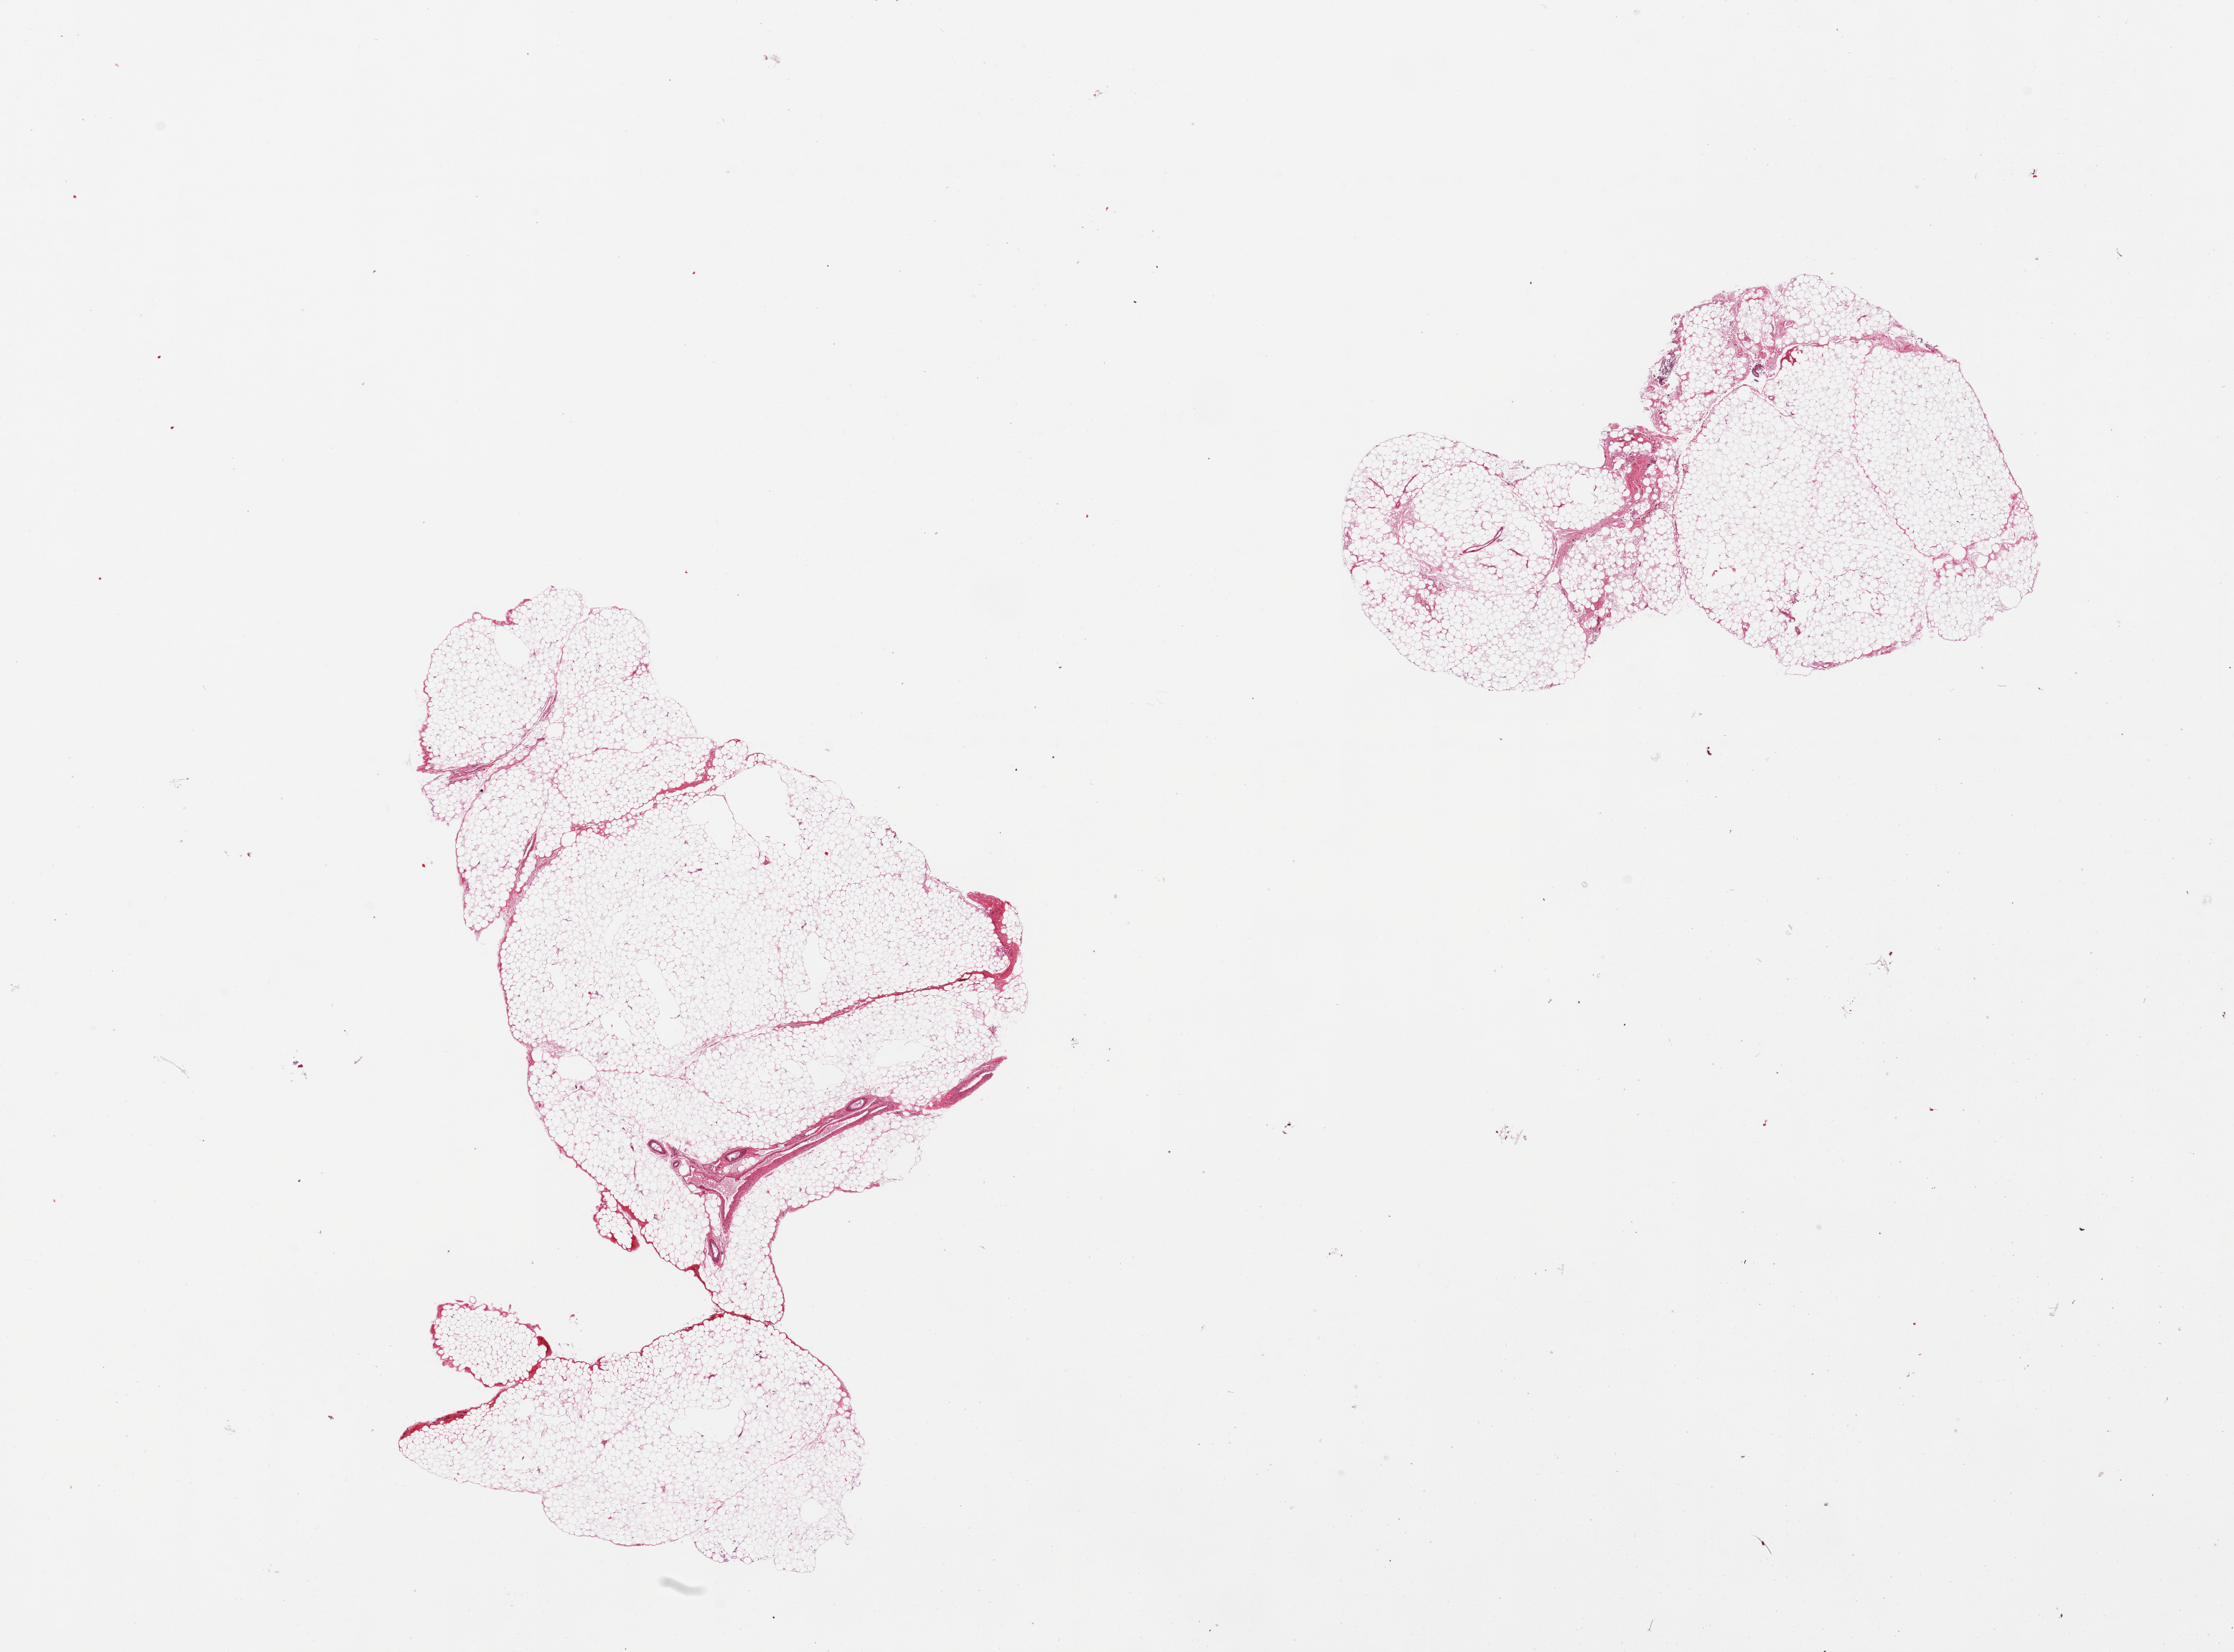
Hematoxylin and eosin (H&E) whole-slide image — a low-resolution overview of the entire scanned area, about 24.6 x 18.2 mm; PAXgene-fixed, paraffin-embedded tissue; section of omentum (target tissue); donor tissue sample. Donor: female.
• review note (as recorded): 2 pieces, minimal (~5%) vessel/fibrous tissue